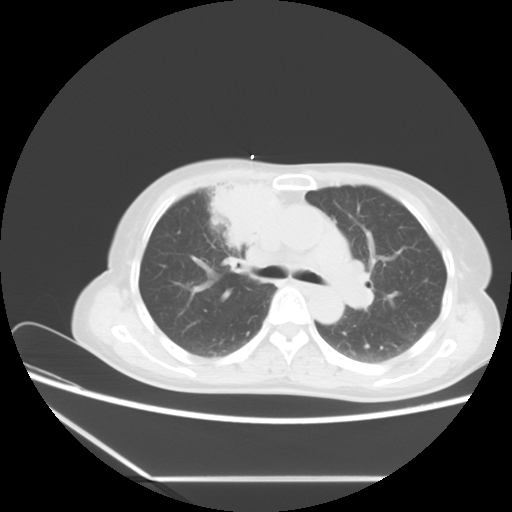
Chest CT, one axial slice; position 12 of 16 along the scan axis; reconstruction kernel STANDARD; 120 kVp; lung window (W 1500 / L -600 HU); 5 mm slice thickness; 512 × 512 image matrix. Female patient, age 63 years. Case-level facts recorded for this patient, not image findings: clinical TNM (as recorded): T2b N1 M0.
Annotated regions visible in this slice (bounding box drawn by a radiologist):
- lung tumour (recorded histology: adenocarcinoma): bounding box <200,168,276,261> (left, top, right, bottom; pixels)